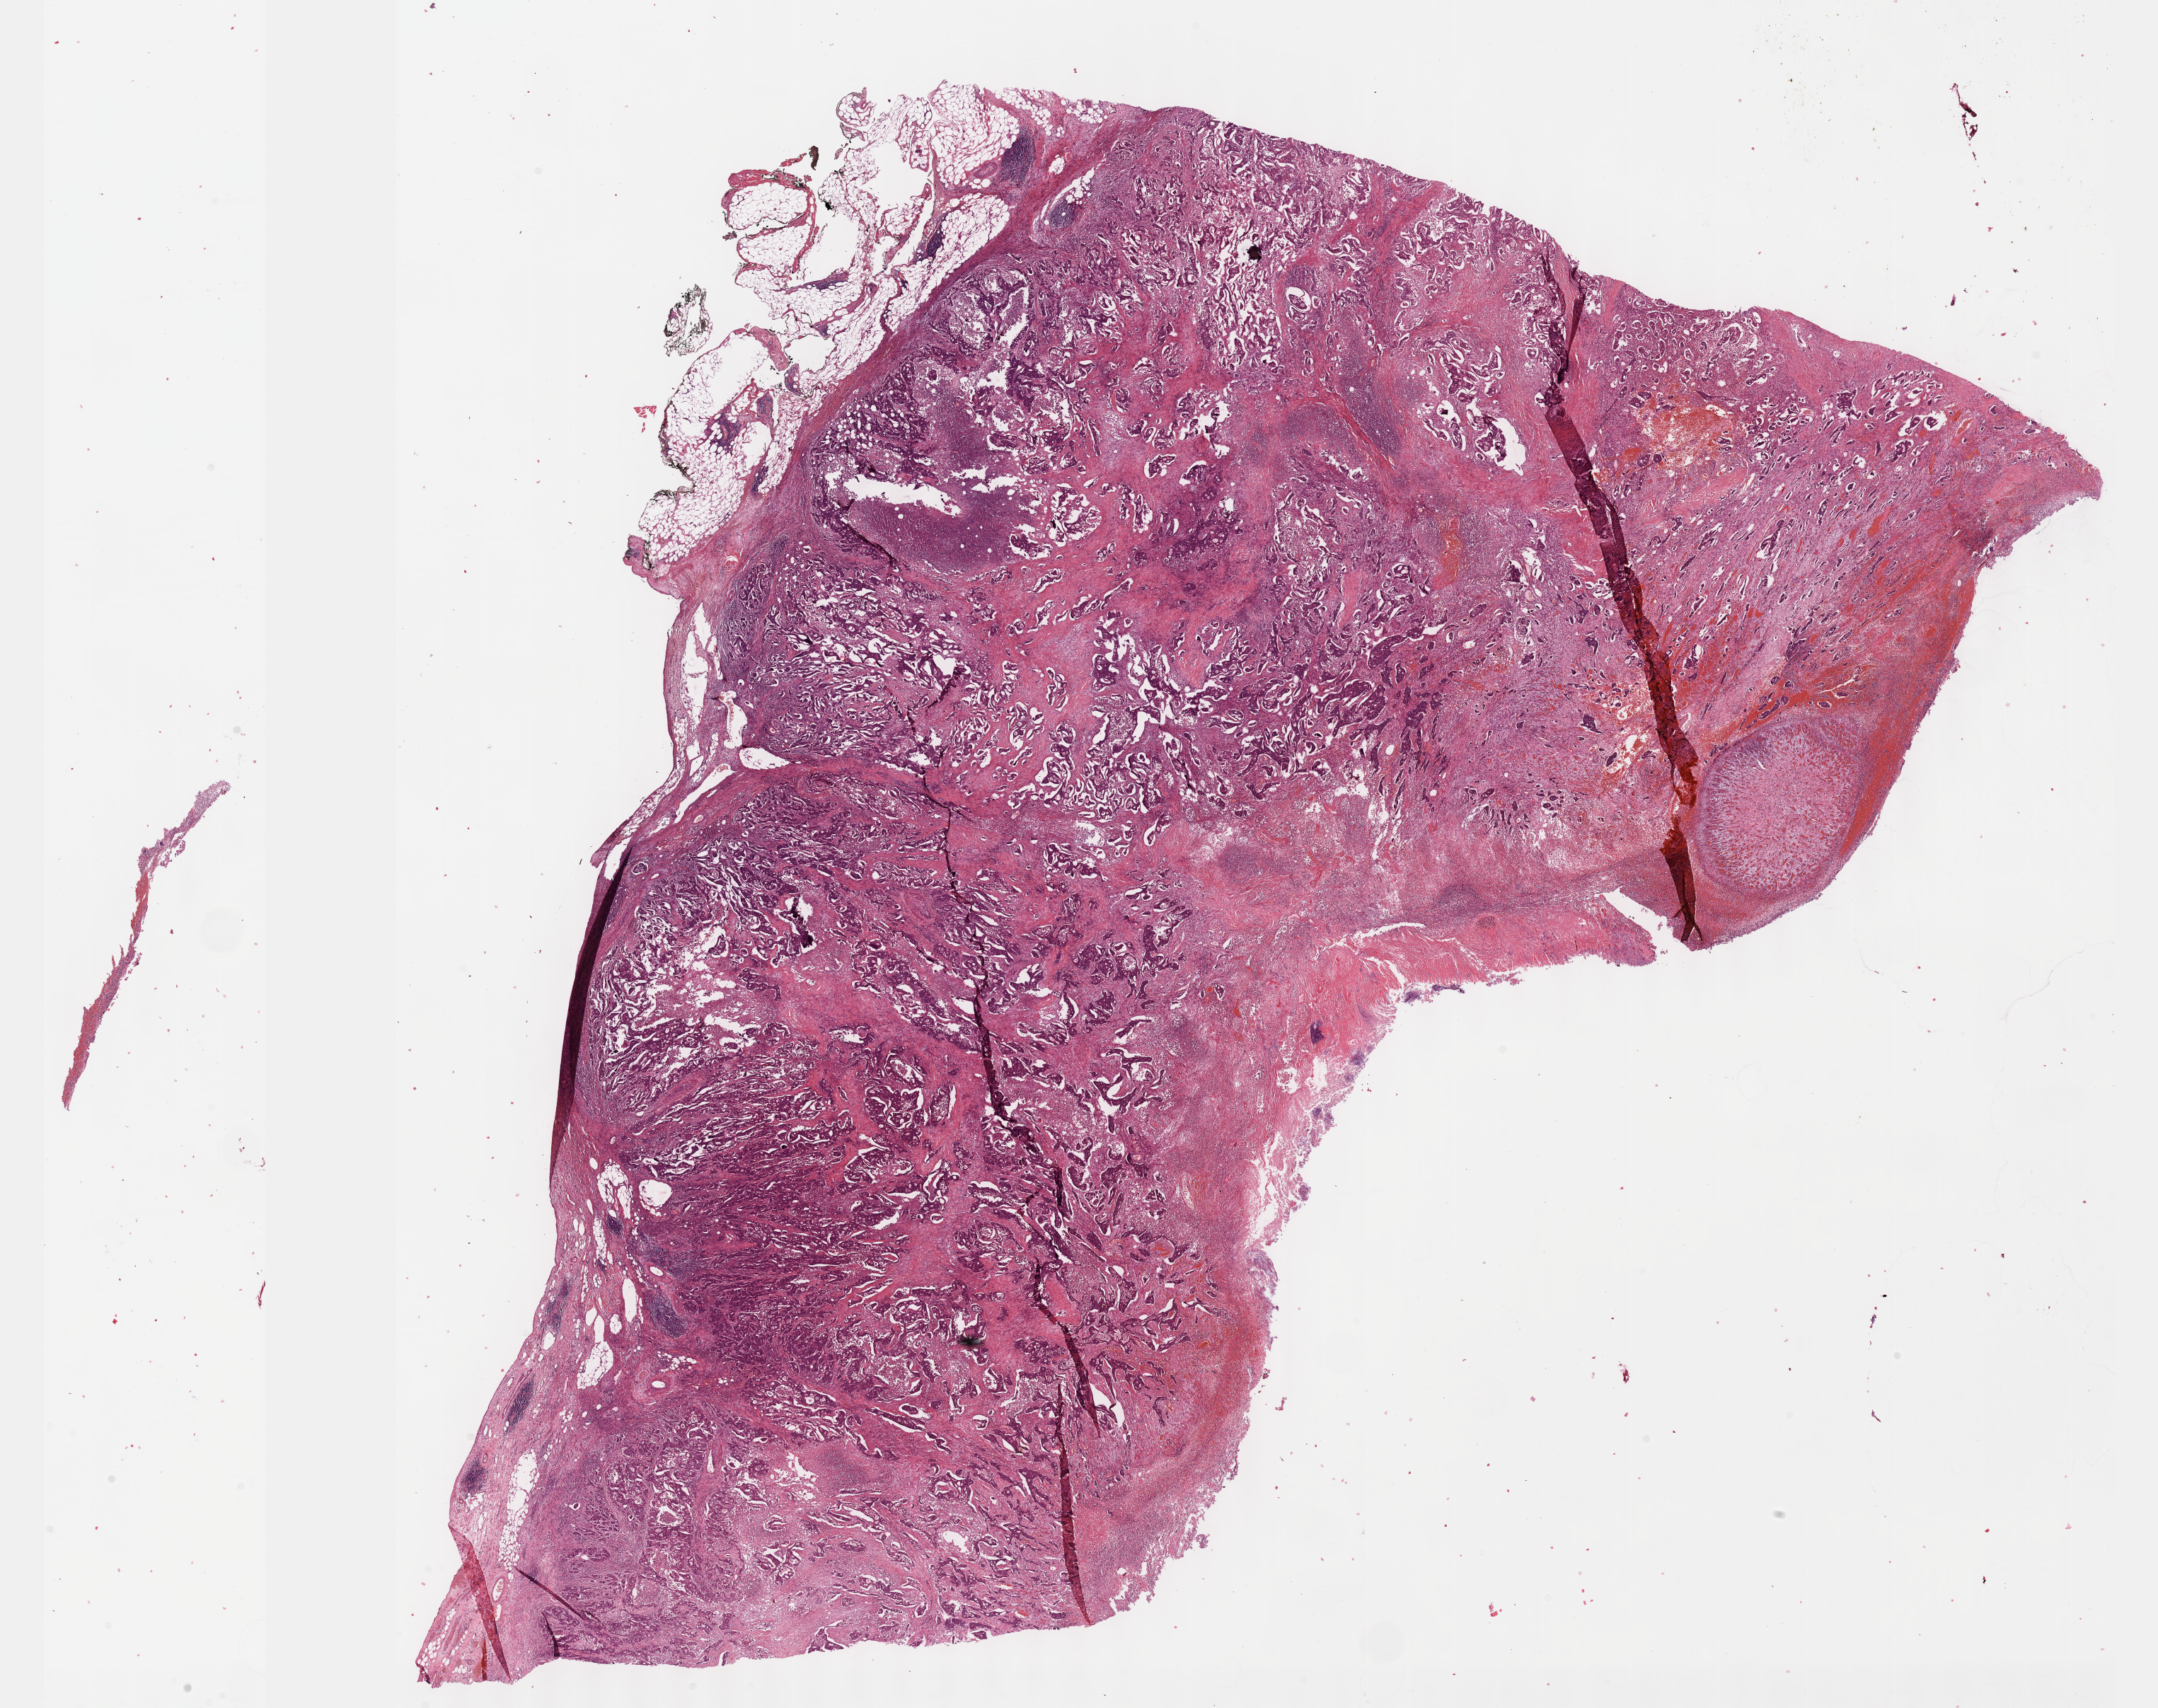
Digitized H&E-stained tissue section (whole slide) — shown as a low-resolution overview of the whole scanned area (about 24.6 x 19.5 mm, acquisition: 40x scan). Formalin-fixed paraffin-embedded (FFPE) diagnostic section. Sample: primary tumour, stomach. Male, age 76 years at initial diagnosis. Histologic grade: G2 (moderately differentiated).
AJCC pathologic stage: IV (6th edition). Diagnosis: Tubular adenocarcinoma (body of stomach). Lymph nodes positive (case pathology): 3 of 19 examined.